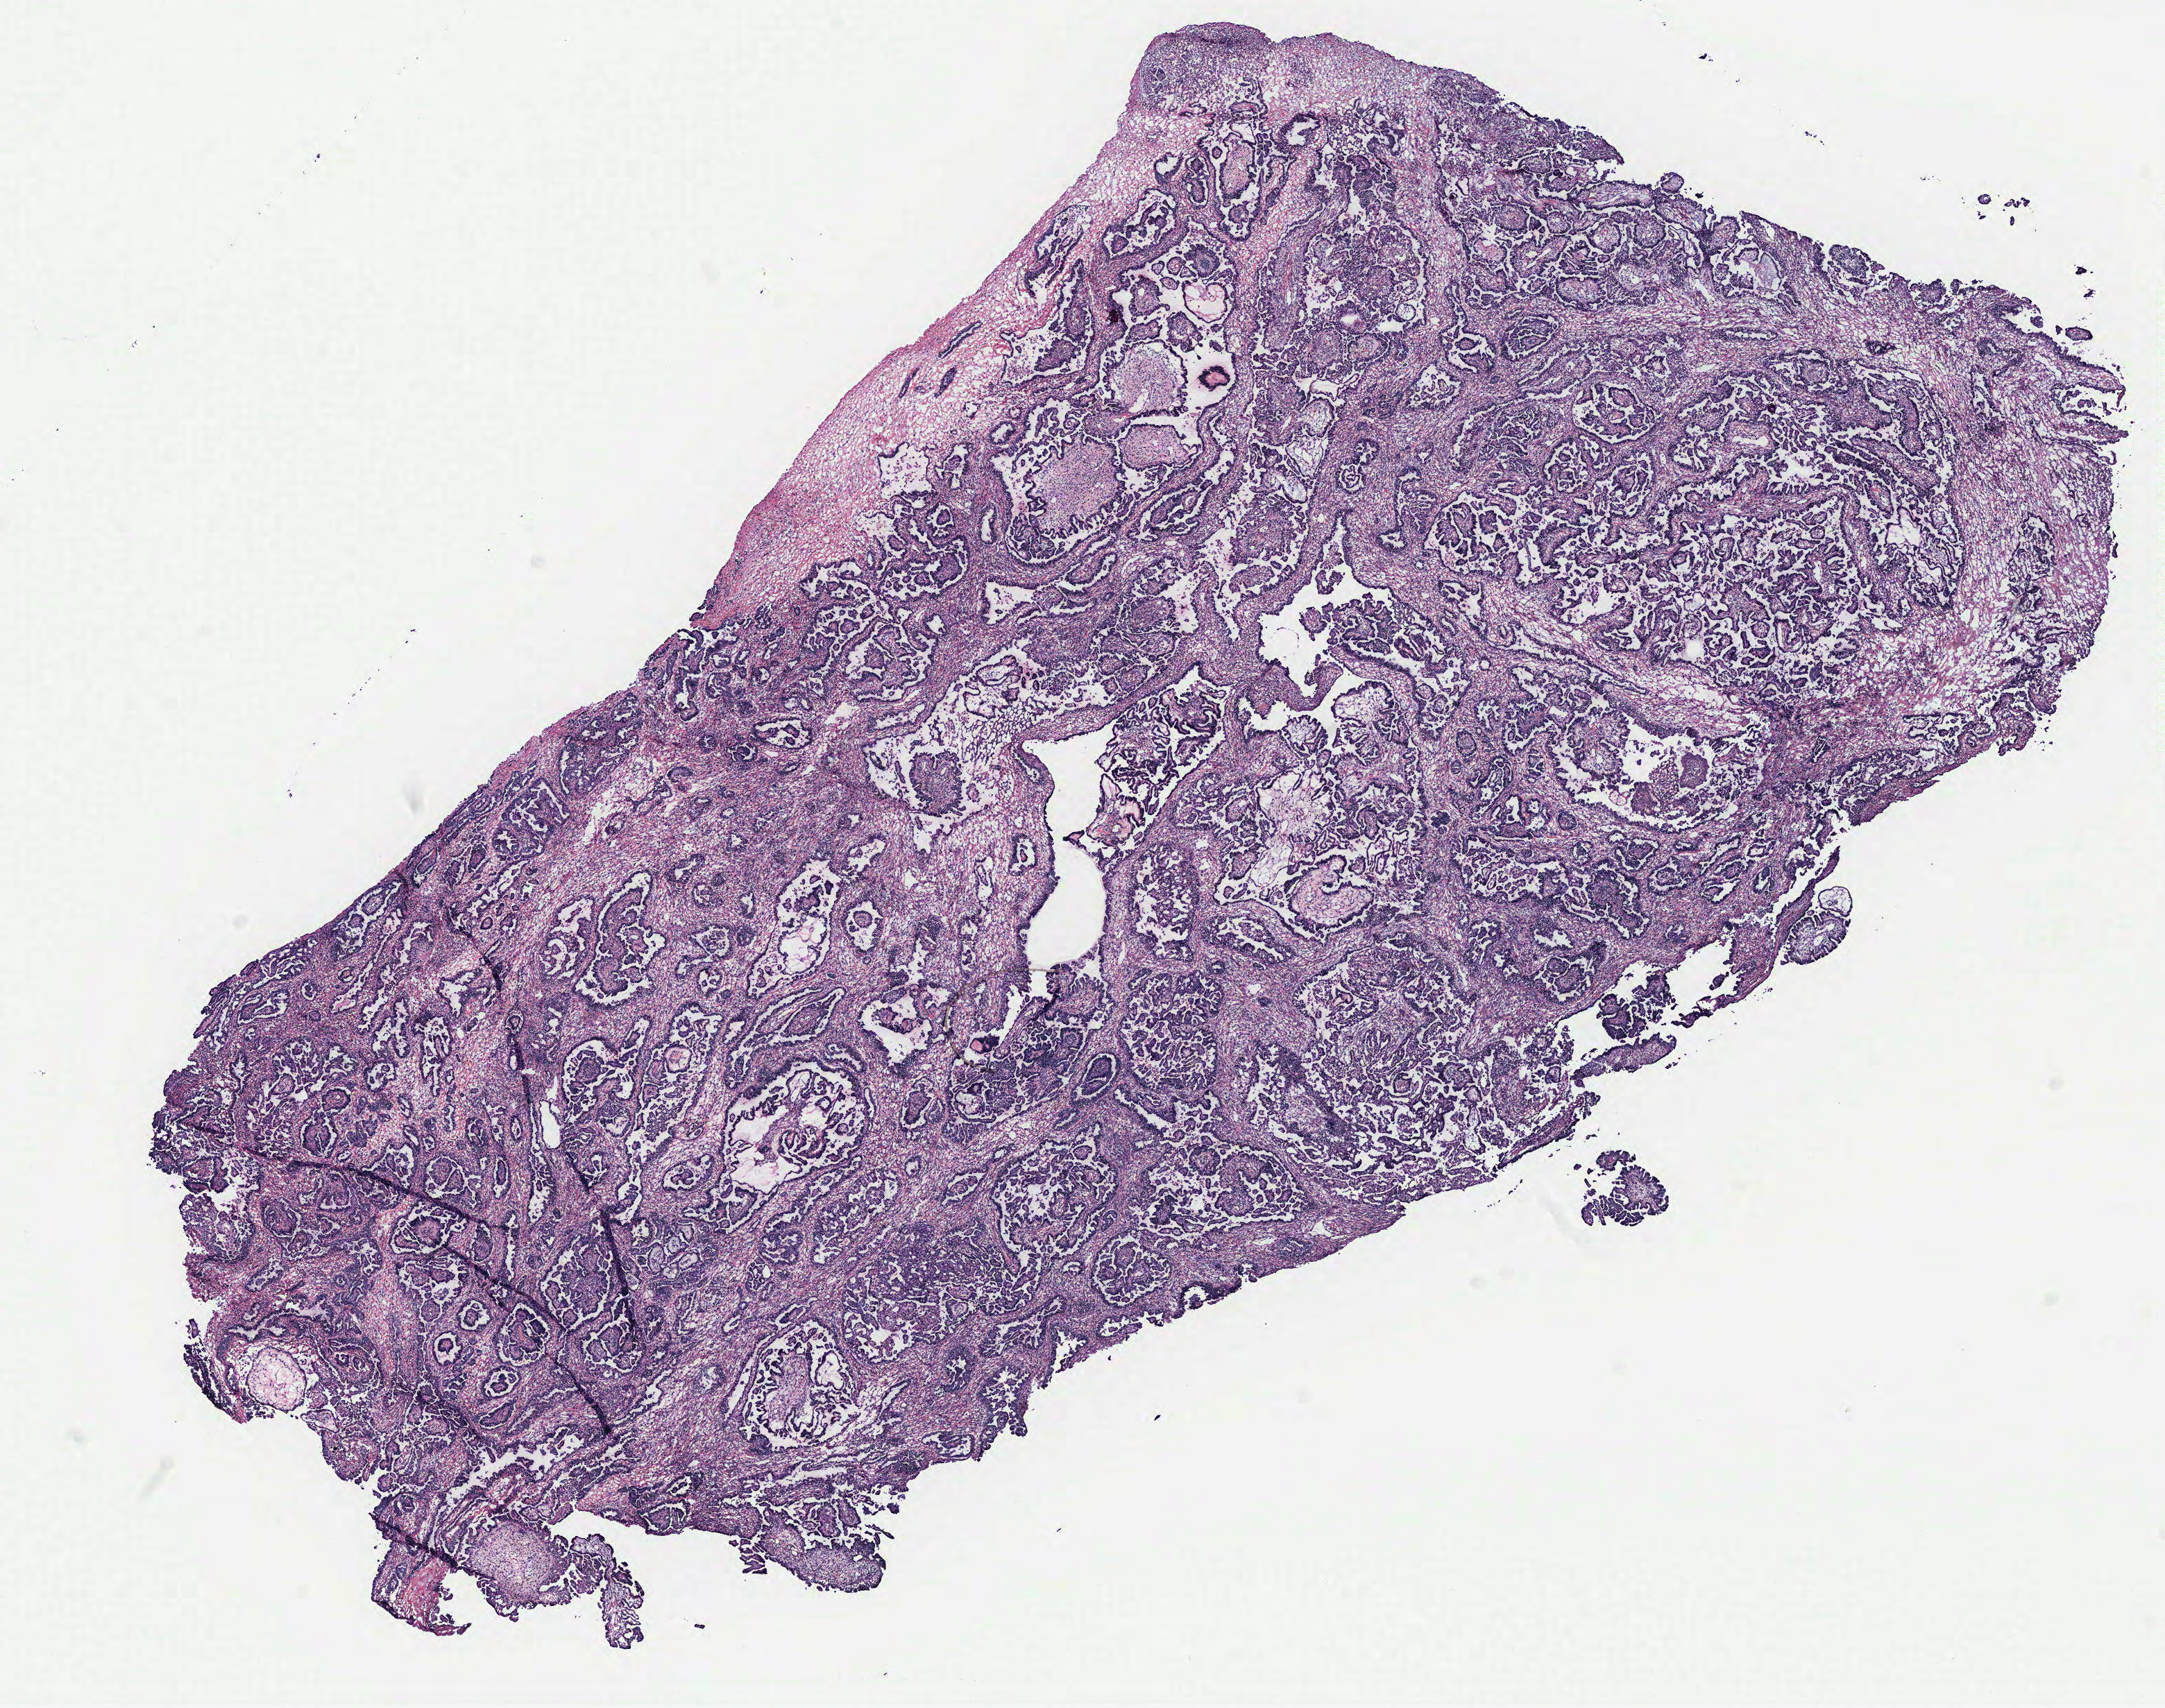
H&E-stained whole-slide image — a low-resolution overview of the entire scanned area, about 12.5 x 9.9 mm (acquisition: 40x scan); ovary, tumour tissue. Female, 46 y/o.
Primary tumour site (as recorded): ovary. Histologic diagnosis: Serous adenocarcinoma, NOS.